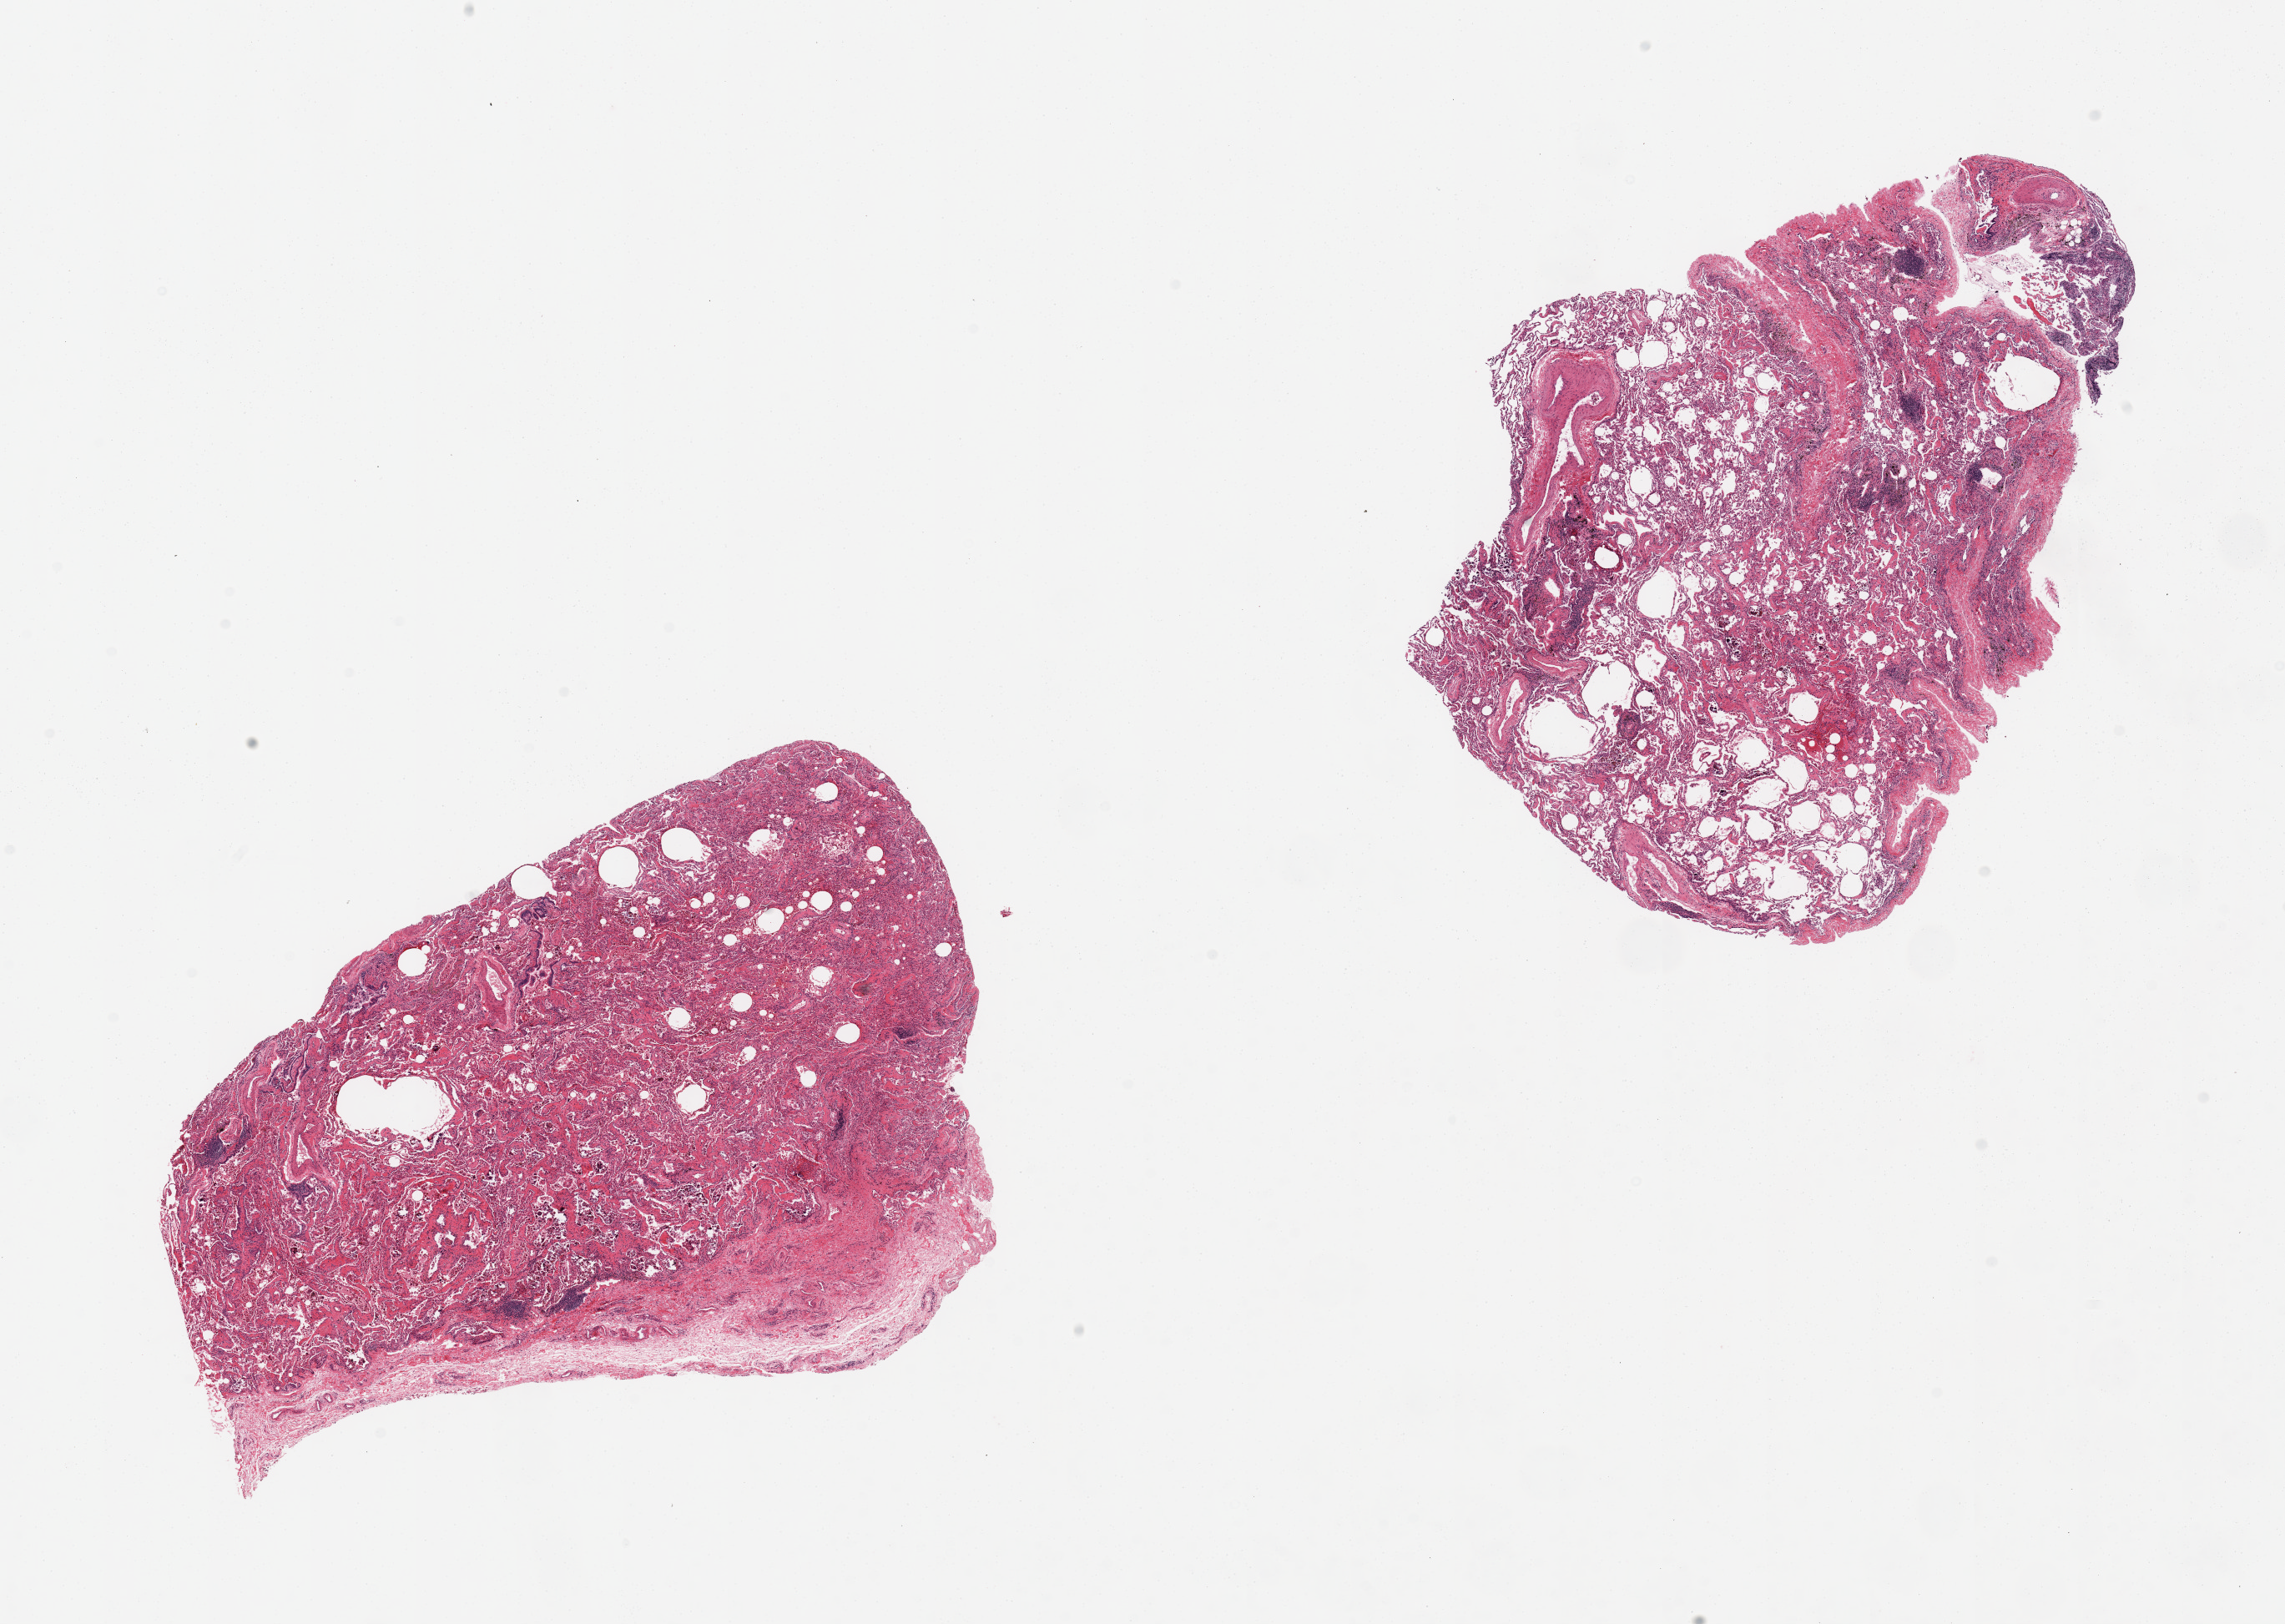
Haematoxylin and eosin whole-slide image, whole scanned area (about 21.7 x 15.4 mm, from a 20x scan) shown as a low-resolution overview; PAXgene-fixed paraffin-embedded (PFPE) section; target tissue: lung; tissue donor sample. Male donor.
Pathologist's review note for this sample: 2 pieces; thickening of the alveolar walls (fibrossi) with accumulation of a large number of mononuclear cells and hemosiderinophages; patchy lymphocytic interstitial infiltrates with associated hemosiderinophages; one piece contains thickened visceral pleura marked).